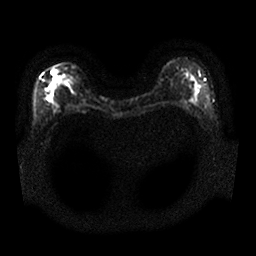
Breast MRI, one axial slice; diffusion-weighted series; image 2 of 4 stored at this slice position (different b-values; order by instance number); 1.5 T; 4 mm slice thickness; 256 × 256 image matrix, field of view 340 × 340 mm. Female patient.
Structures marked on this image (expert manual segmentation):
- tumour on diffusion-weighted imaging: bounding box (x1, y1, x2, y2) in pixels: (47, 68, 61, 92)